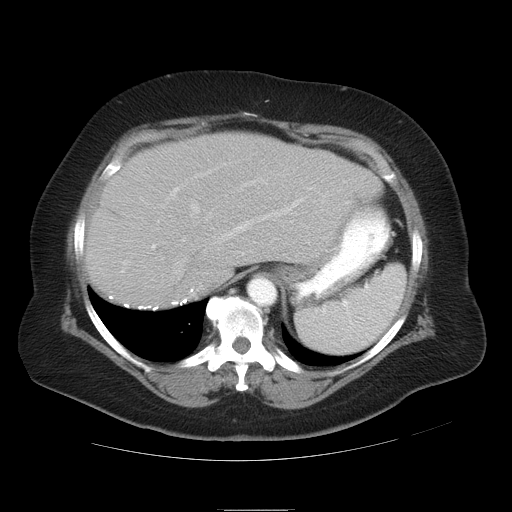
Contrast-enhanced abdominal CT, one axial slice. Slice 28 of 37 in the series (ordered by position). 120 kVp. Intravenous contrast given. Soft-tissue window (W 400 / L 40 HU). 7.5 mm slice thickness. 512 × 512 image matrix, field of view 422 × 422 mm. Female patient, age 68 years. From the clinical record (not read from this slice): diagnosis: colorectal cancer liver metastases, imaged before liver resection.
Outlined on this slice (manually delineated by an expert):
- hepatic veins: bounding box <181,176,275,245> (left, top, right, bottom; pixels)
- liver: <86,133,382,311>
- planned liver remnant (the part of the liver to remain after resection): <87,133,382,310>
- portal vein (with intrahepatic branches): <141,167,304,302>